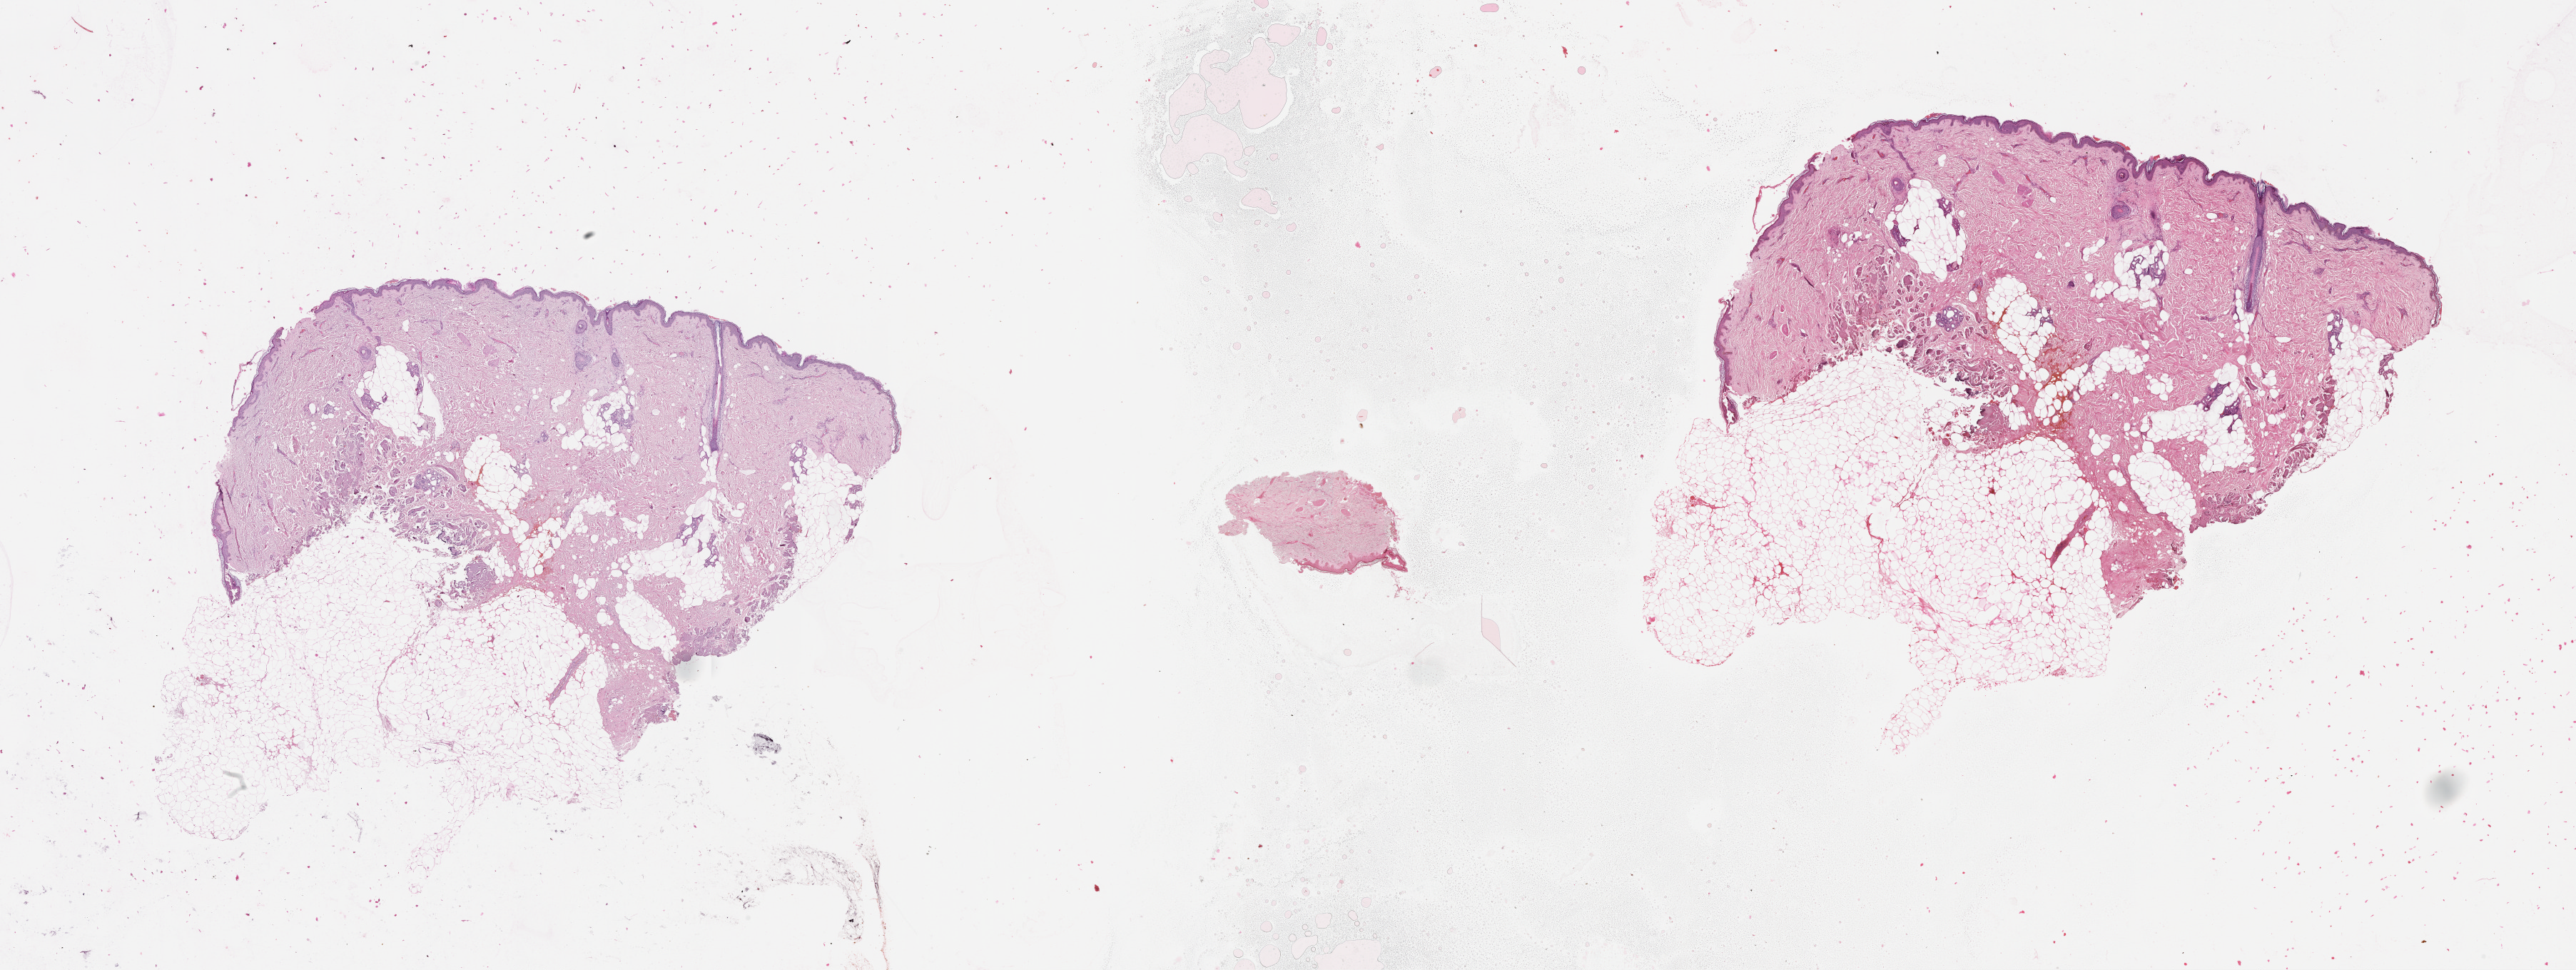
Digitized H&E-stained tissue section (whole slide), shown as a low-resolution overview of the whole scanned area (about 29.1 x 10.9 mm). 55-year-old female patient.
Patient diagnosis: Malignant melanoma, NOS.